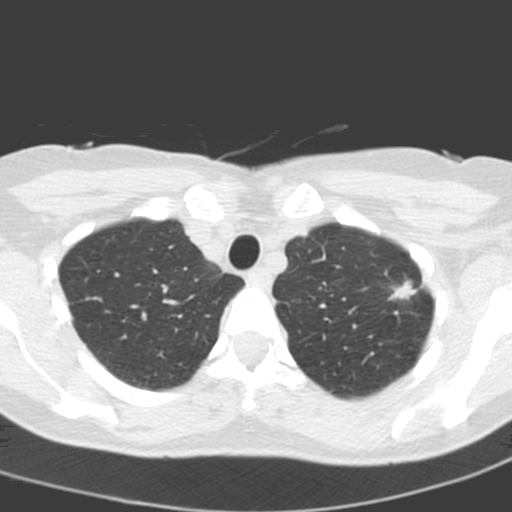
Low-dose screening chest CT, axial slice, baseline annual screen, lung window (W 1500 / L -600 HU), 120 kVp, slice 33 of 193 in the series, 512 × 512 image matrix. Female, age 58 years at enrolment.
• Expert reader's lesion annotation, bounding box (x1, y1, x2, y2) in pixels: (380, 270, 427, 318).
• Reader record for this screening exam (exam-level; its link to the box is not recorded): non-calcified nodule or mass ≥4 mm, left upper lobe, 14 × 10 mm, spiculated (stellate) margins, soft tissue attenuation.
• Official screen result: positive, change unspecified: nodule(s) >= 4 mm or enlarging nodule(s), mass(es), or other non-specific abnormalities suspicious for lung cancer.
• Later outcome: lung cancer diagnosed 48 days after this screen — adenocarcinoma, NOS, left upper lobe, poorly differentiated (G3), stage IA (AJCC 6th edition), 13 mm at pathology.